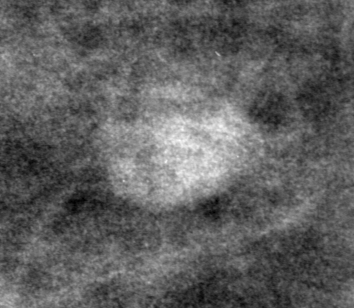
Cropped region of a digitized screen-film mammogram centred on a radiologist-marked abnormality, right breast, CC view, BI-RADS breast density category 1 (scale 1–4).
- Marked abnormality: mass, shape lobulated, margins obscured; BI-RADS assessment category 0 (incomplete: needs additional imaging); subtlety rating 4 on a 1 (subtle) to 5 (obvious) scale; pathology result (as recorded, not read from the image): benign.